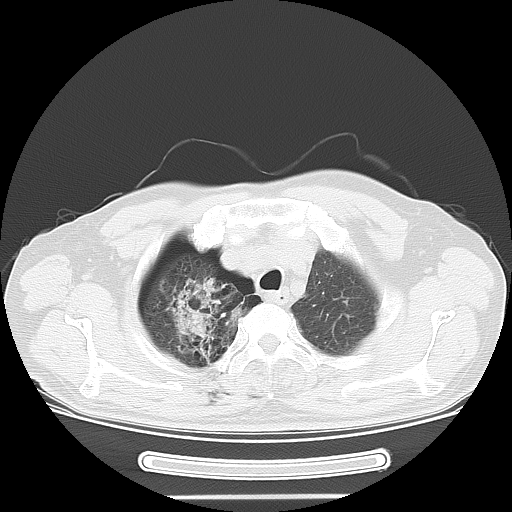
Chest CT, one axial slice. Position 49 of 57 along the scan axis. 120 kVp. Lung window (W 1500 / L -600 HU). 5 mm slice thickness. 512 × 512 image matrix, field of view 376 × 376 mm. Patient: male, 61 years. Case-level facts recorded for this patient, not image findings: clinical TNM (as recorded): T1c N3 M1b.
Outlined on this slice (rectangle marked by the reading radiologist):
- lung tumour (recorded histology: adenocarcinoma): bounding box [x1, y1, x2, y2] px = [156, 270, 256, 367]